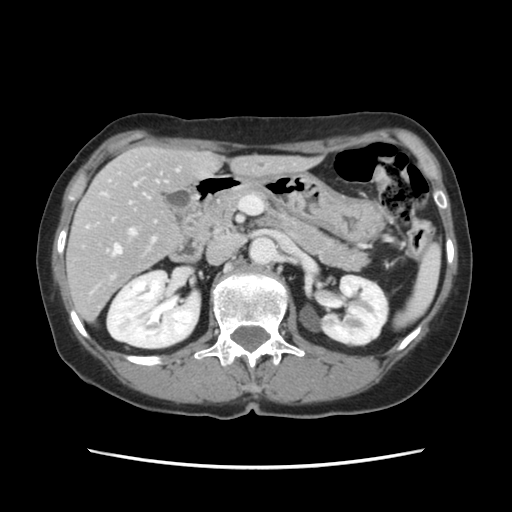
Contrast-enhanced abdominal CT, one axial slice; position 61 of 120 along the scan axis; 120 kVp; intravenous contrast given; soft-tissue window (W 400 / L 40 HU); 2.5 mm slice thickness; 512 × 512 image matrix, field of view 330 × 330 mm. Female patient, age 70 years. Case-level facts recorded for this patient, not image findings: diagnosis: colorectal cancer liver metastases, imaged before liver resection; multiple liver metastases: no; largest metastasis: 2.5 cm; disease in both lobes: no.
Annotated regions visible in this slice (manually delineated by an expert):
- hepatic veins: bounding box <87,181,158,255> (left, top, right, bottom; pixels)
- liver: <68,147,307,320>
- planned liver remnant (the part of the liver to remain after resection): <71,147,307,286>
- portal vein (with intrahepatic branches): <103,169,179,241>